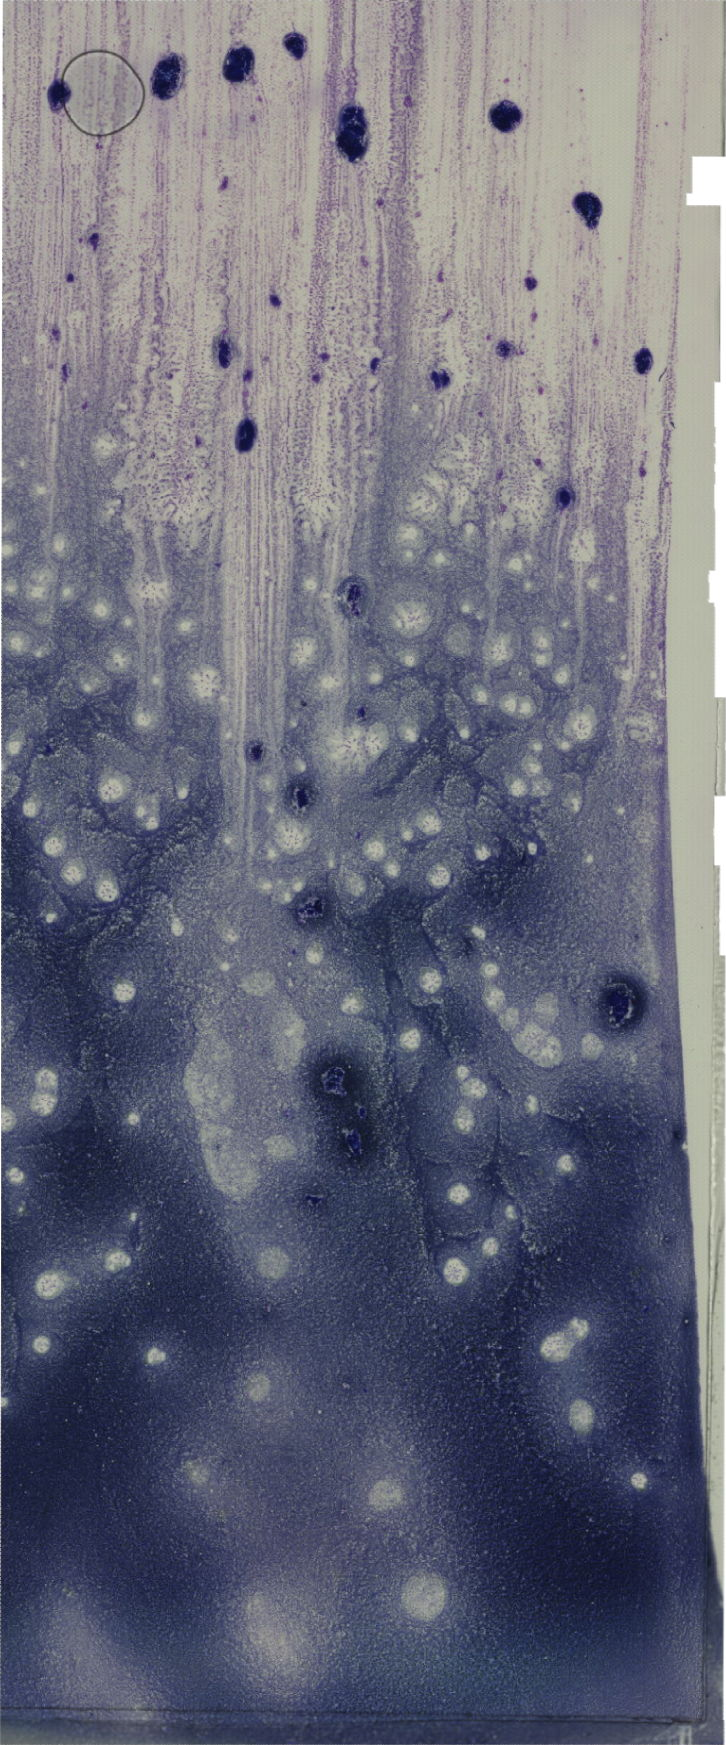
Whole-slide image of a May-Grünwald-Giemsa (MGG)-stained bone marrow aspirate smear — whole scanned area (about 20.6 x 49.5 mm) shown as a low-resolution overview. Female patient.
• diagnosis: Mixed Phenotype Acute Leukemia, B/Myeloid